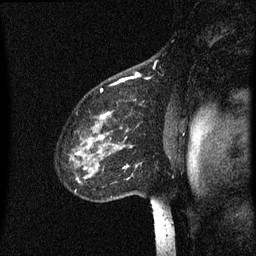
Breast MRI (dynamic contrast-enhanced), one sagittal slice. Slice 48 of 60 in the series (ordered by position). Dynamic contrast-enhanced series, image 2 of 3 at this slice position (ordered by acquisition). 1.5 T. TE 4.2 ms, TR 8 ms. 256 × 256 image matrix. Female patient, age 60 years.
Annotated regions visible in this slice (semi-automatic segmentation, software-assisted and operator-edited):
- analysis volume of interest (the breast-tissue region the enhancement analysis was run in; not a lesion): bounding box [x1, y1, x2, y2] px = [70, 112, 145, 197]
- tumour enhancement mask (voxels above the 70 % enhancement threshold inside the analysis volume of interest): [101, 114, 126, 169]